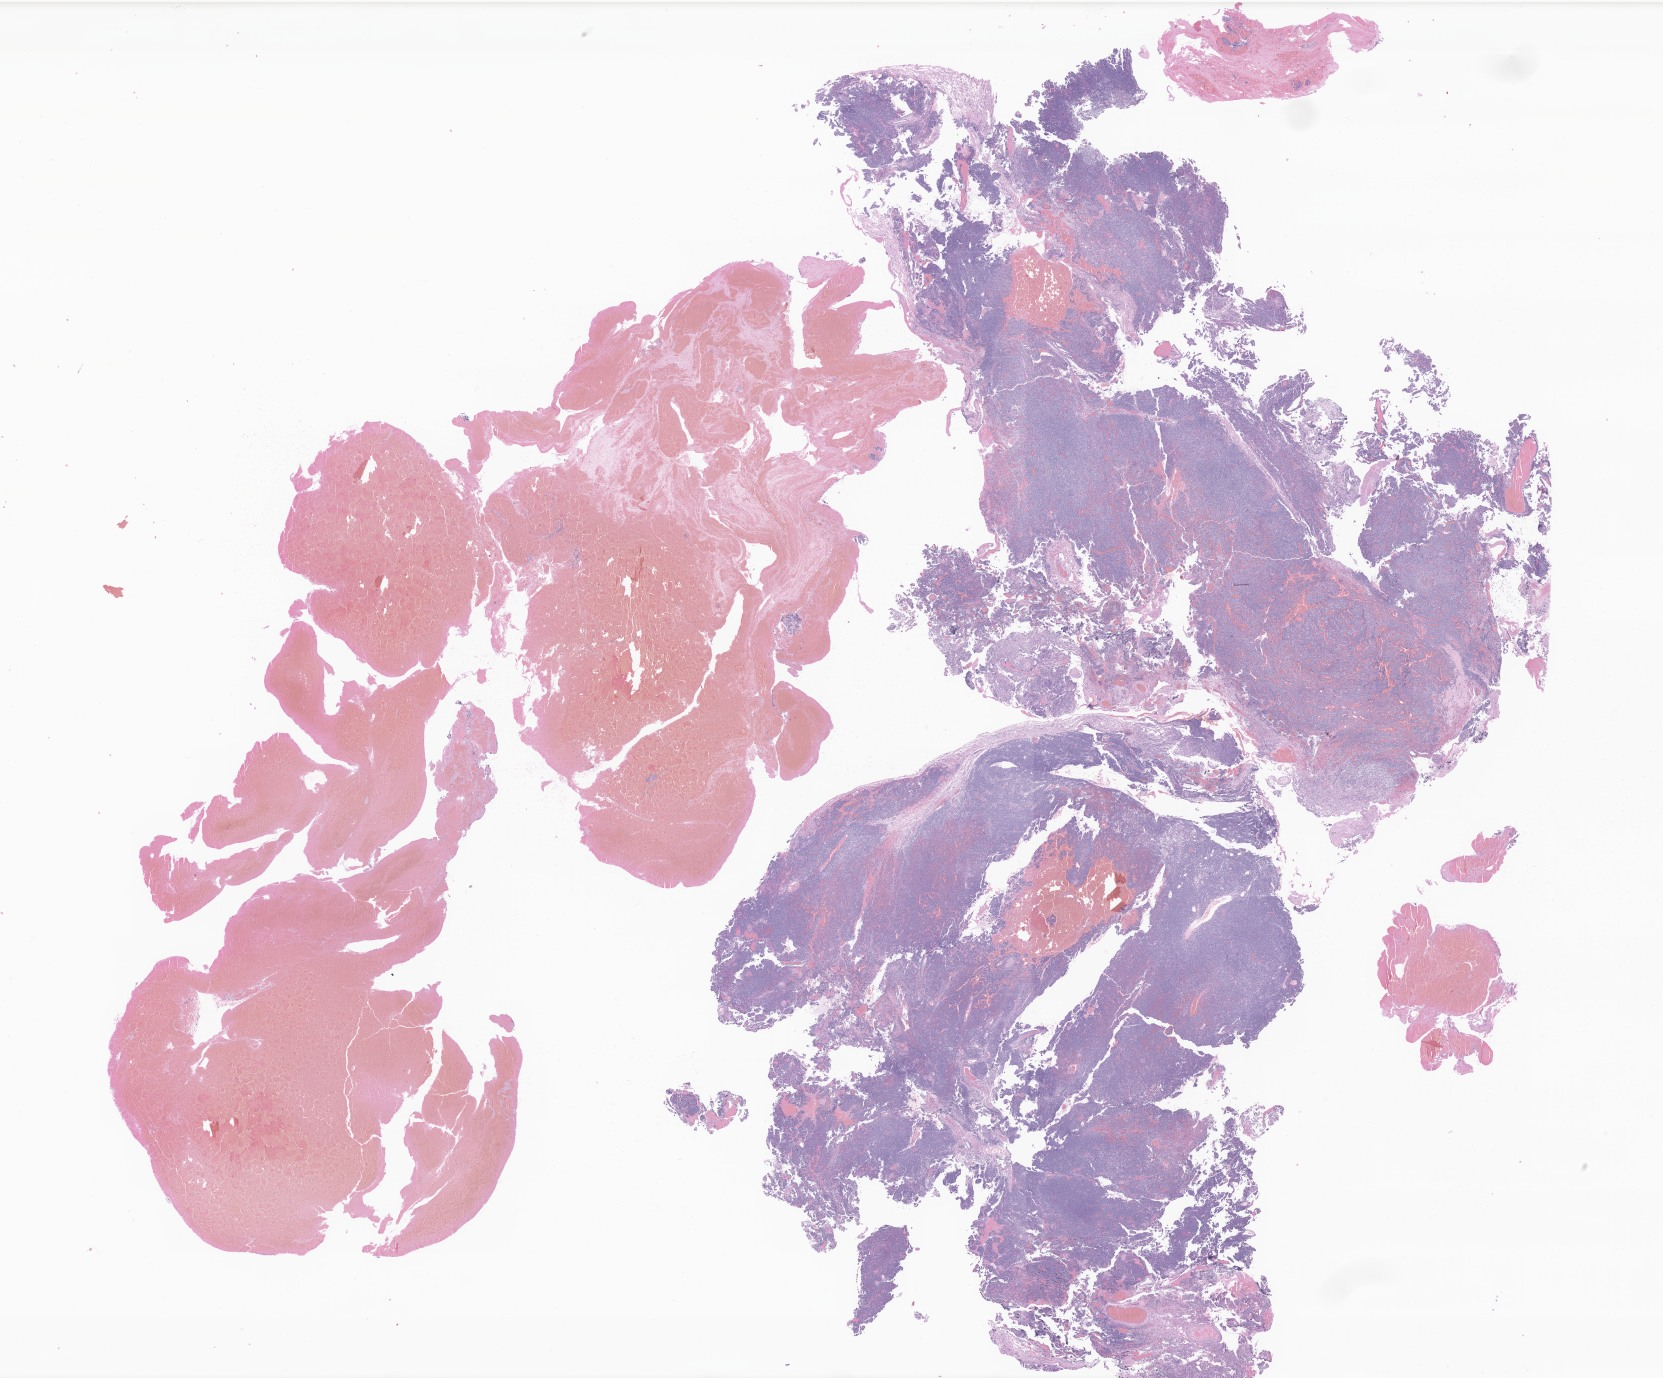
Whole-slide image, H&E stain of tumor tissue from the brain — a low-resolution overview of the entire scanned area, about 28.0 x 23.2 mm, FFPE section. Patient male; age 79 months (6 years 7 months).
Recorded diagnosis: Pilocytic astrocytoma.